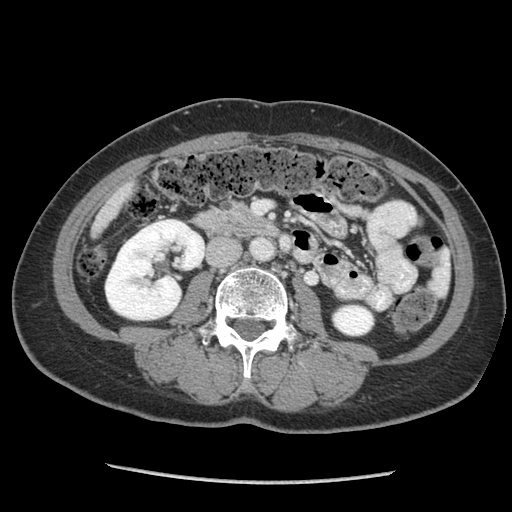
Contrast-enhanced abdominal CT (liver protocol), one axial slice. Slice 15 of 105 in the series (ordered by position). Reconstruction kernel STANDARD. 140 kVp. Soft-tissue window (W 400 / L 40 HU). 512 × 512 image matrix. Case-level facts recorded for this patient, not image findings: diagnosis: hepatocellular carcinoma (patient treated with transarterial chemoembolisation; whether this scan precedes or follows treatment is not stated here); TNM stage (as recorded): Stage-I; Child-Pugh class: A; tumour differentiation: moderately differentiated.
Annotated regions visible in this slice (semi-automatic segmentation, software-assisted and operator-edited):
- liver parenchyma outside the tumour (the mass and vessels are separate outlines, so this box may not span the whole liver): bounding box [x1, y1, x2, y2] px = [92, 180, 134, 237]